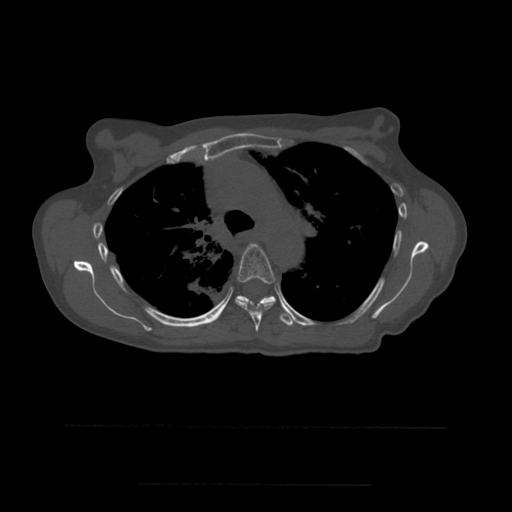
CT including the spine, one axial slice; position 388 of 544 along the scan axis; bone window (W 1800 / L 400 HU); 512 × 512 image matrix. Patient age 58 years. Case-level facts recorded for this patient, not image findings: primary cancer: lung.
Structures marked on this image (semi-automatically segmented with operator editing):
- T5 vertebra: bounding box (x1, y1, x2, y2) in pixels: (236, 244, 276, 332)
- T6 vertebra: (236, 295, 296, 327)